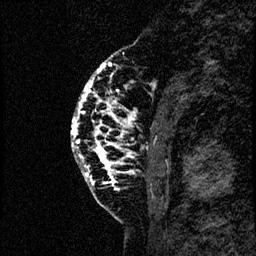
Breast MRI (dynamic contrast-enhanced), one sagittal slice; slice 19 of 60 in the series (ordered by position); dynamic contrast-enhanced study with each time point stored as its own series, time point 2 of 4 at this slice position (early post-contrast, ordered by acquisition time); 1.5 T; TE 4.2 ms, TR 17.6 ms; 2 mm slice thickness; 256 × 256 image matrix. Female patient, age 40 years. Case-level facts recorded for this patient, not image findings: setting: breast cancer imaged before/during neoadjuvant chemotherapy; receptor status: HER2-positive.
Structures marked on this image (semi-automatic segmentation, software-assisted and operator-edited):
- analysis volume of interest (the breast-tissue region the enhancement analysis was run in; not a lesion): bounding box [x1, y1, x2, y2] px = [67, 55, 185, 206]
- tumour enhancement mask (voxels above the 100 % enhancement threshold inside the analysis volume of interest): [71, 63, 132, 184]